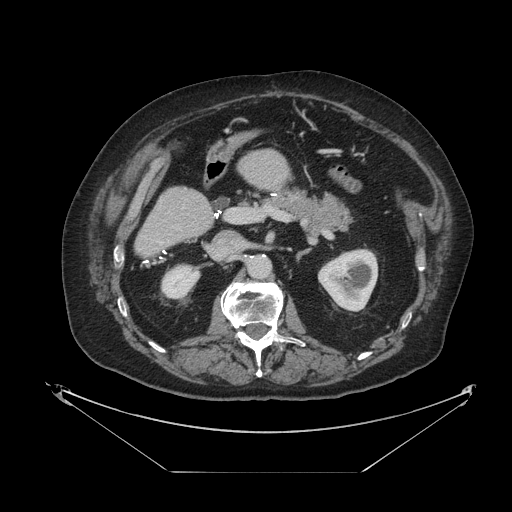
Contrast-enhanced abdominal CT, one axial slice; slice 44 of 121 in the series (ordered by position); soft-tissue window (W 400 / L 40 HU); 2.5 mm slice thickness; 512 × 512 image matrix, field of view 500 × 500 mm. Male patient, age 68 years. Case-level facts recorded for this patient, not image findings: diagnosis: colorectal cancer liver metastases, imaged before liver resection; multiple liver metastases: no; largest metastasis: 4 cm; disease in both lobes: no.
Annotated regions visible in this slice (expert manual segmentation):
- liver: bounding box [x1, y1, x2, y2] px = [136, 150, 290, 255]
- planned liver remnant (the part of the liver to remain after resection): [136, 150, 290, 255]